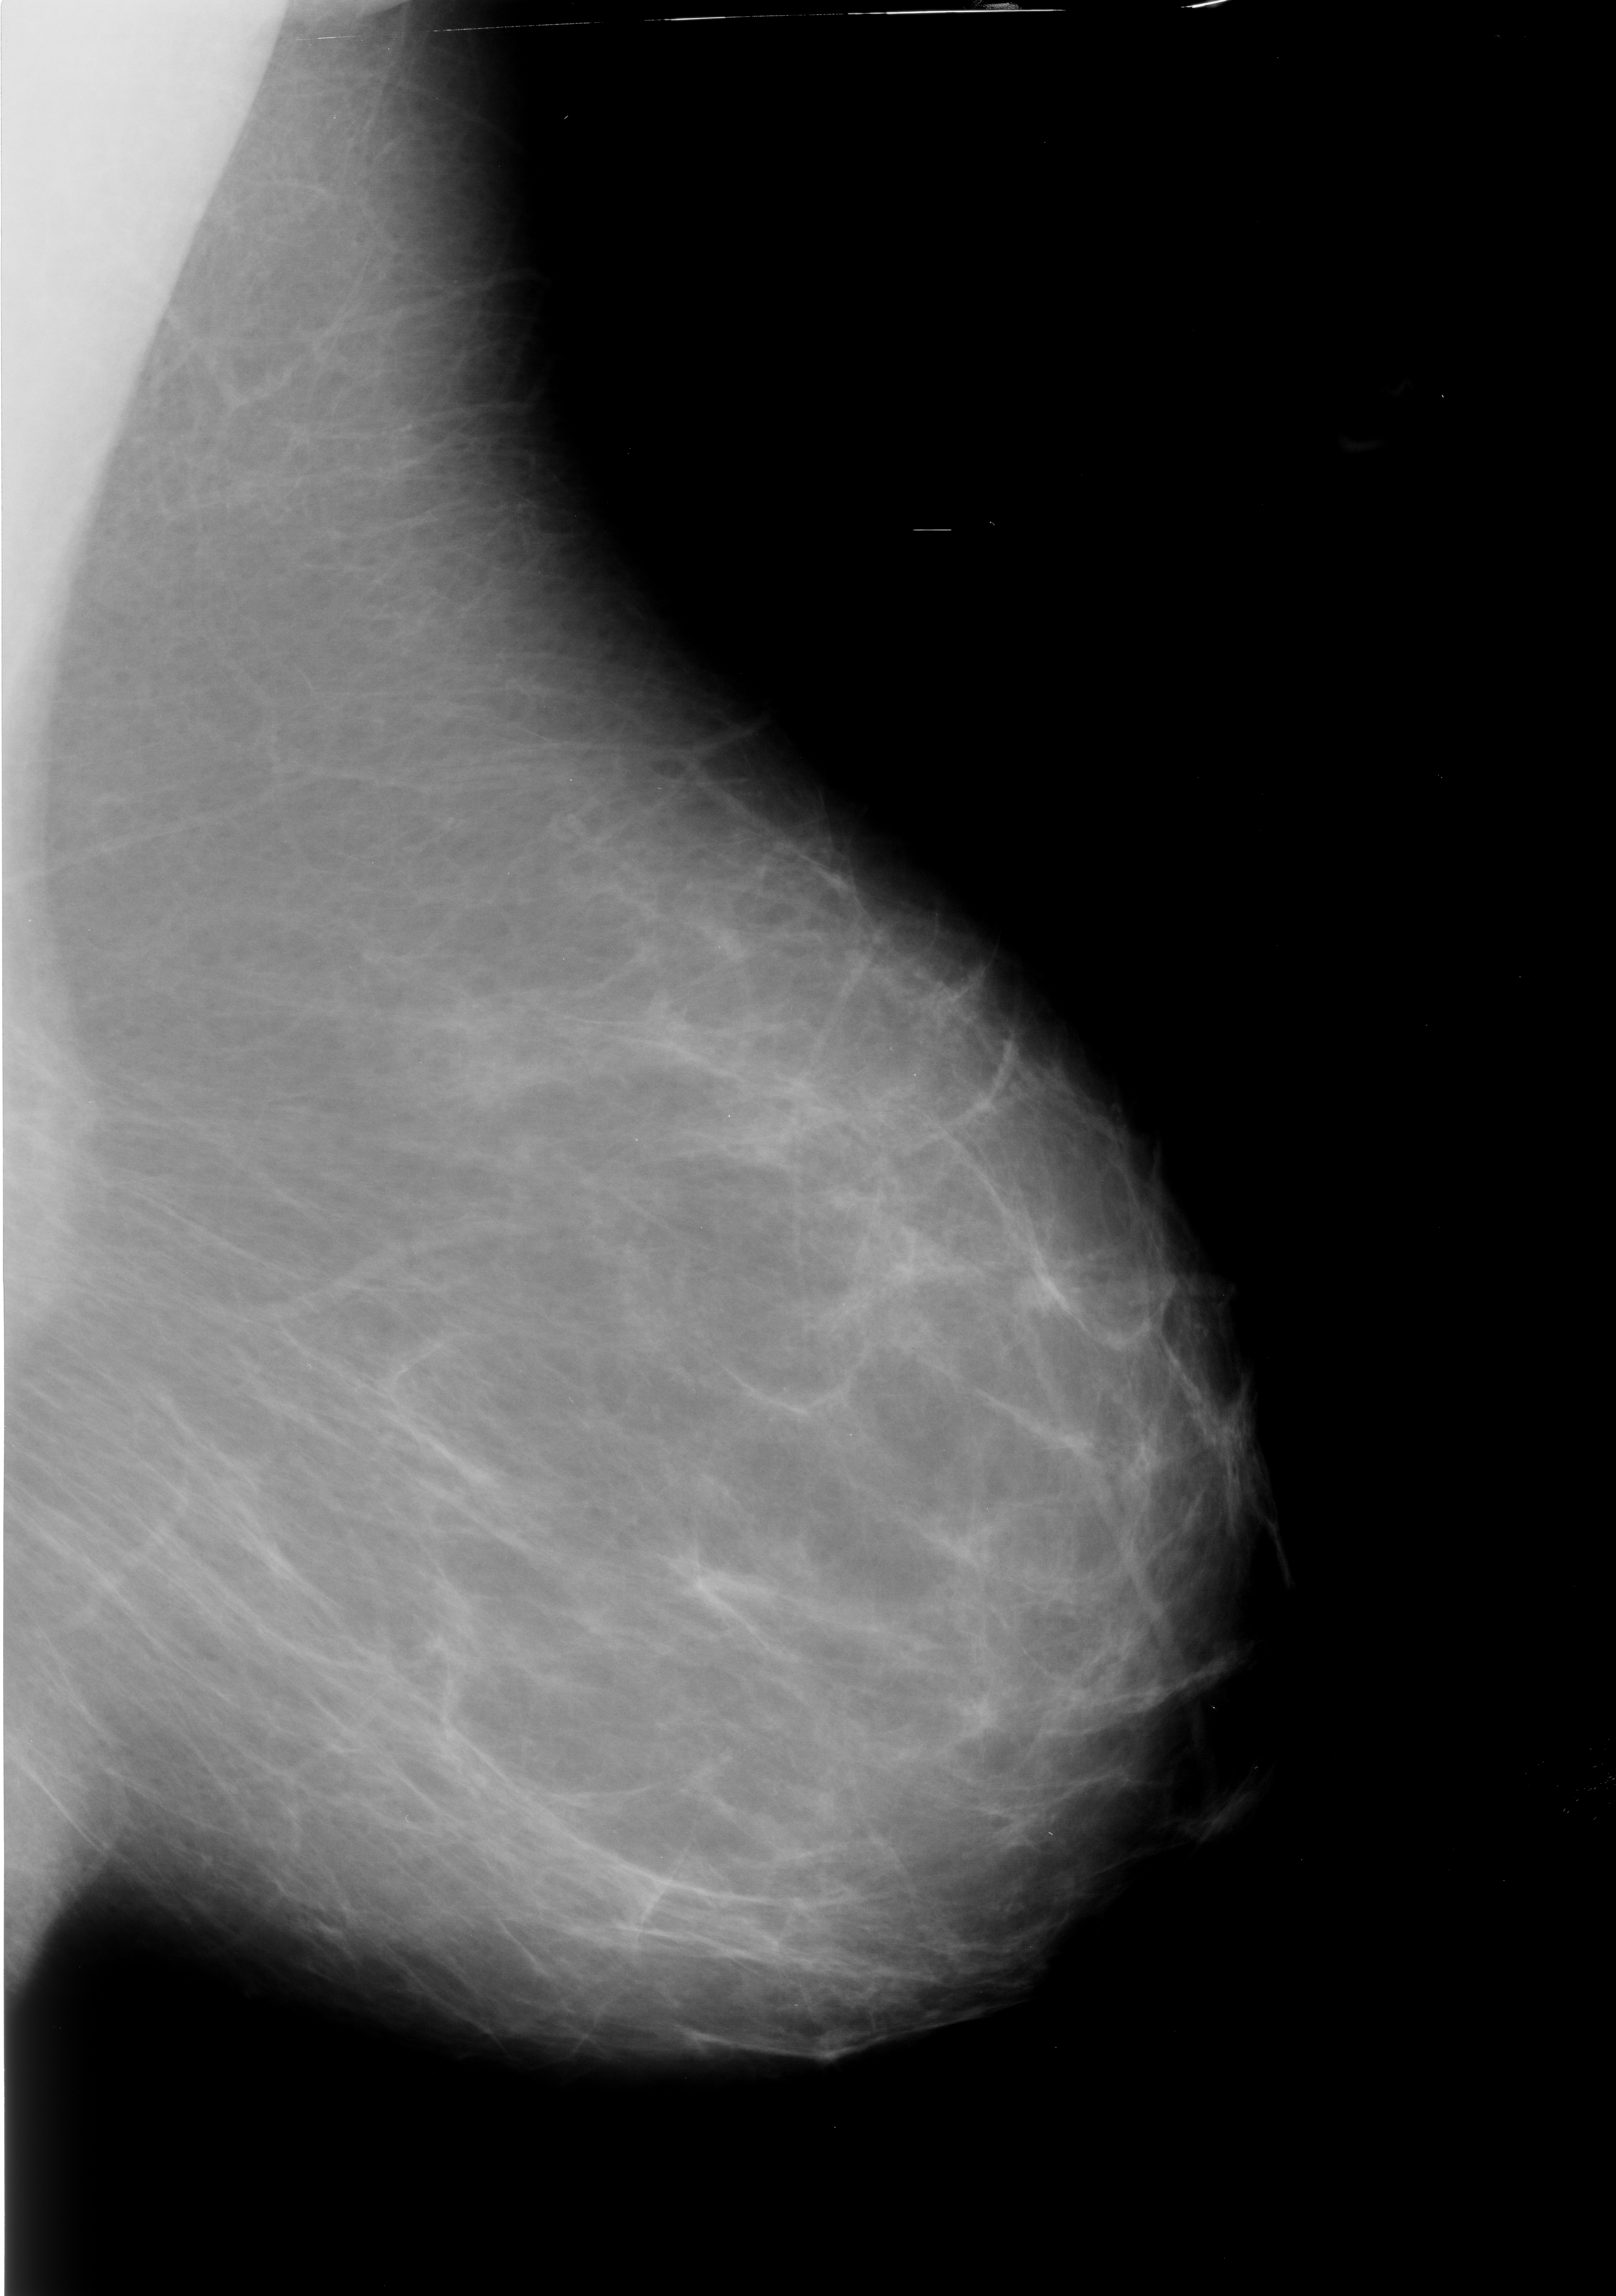
Scanned film-screen mammogram, left breast, MLO view, breast composition: almost entirely fatty (BI-RADS density category 1 of 4).
Marked findings (only marked abnormalities are described; nothing is implied about the rest of the image): mass, shape irregular, margins spiculated; BI-RADS assessment category 4; pathology result (as recorded, not read from the image): malignant.